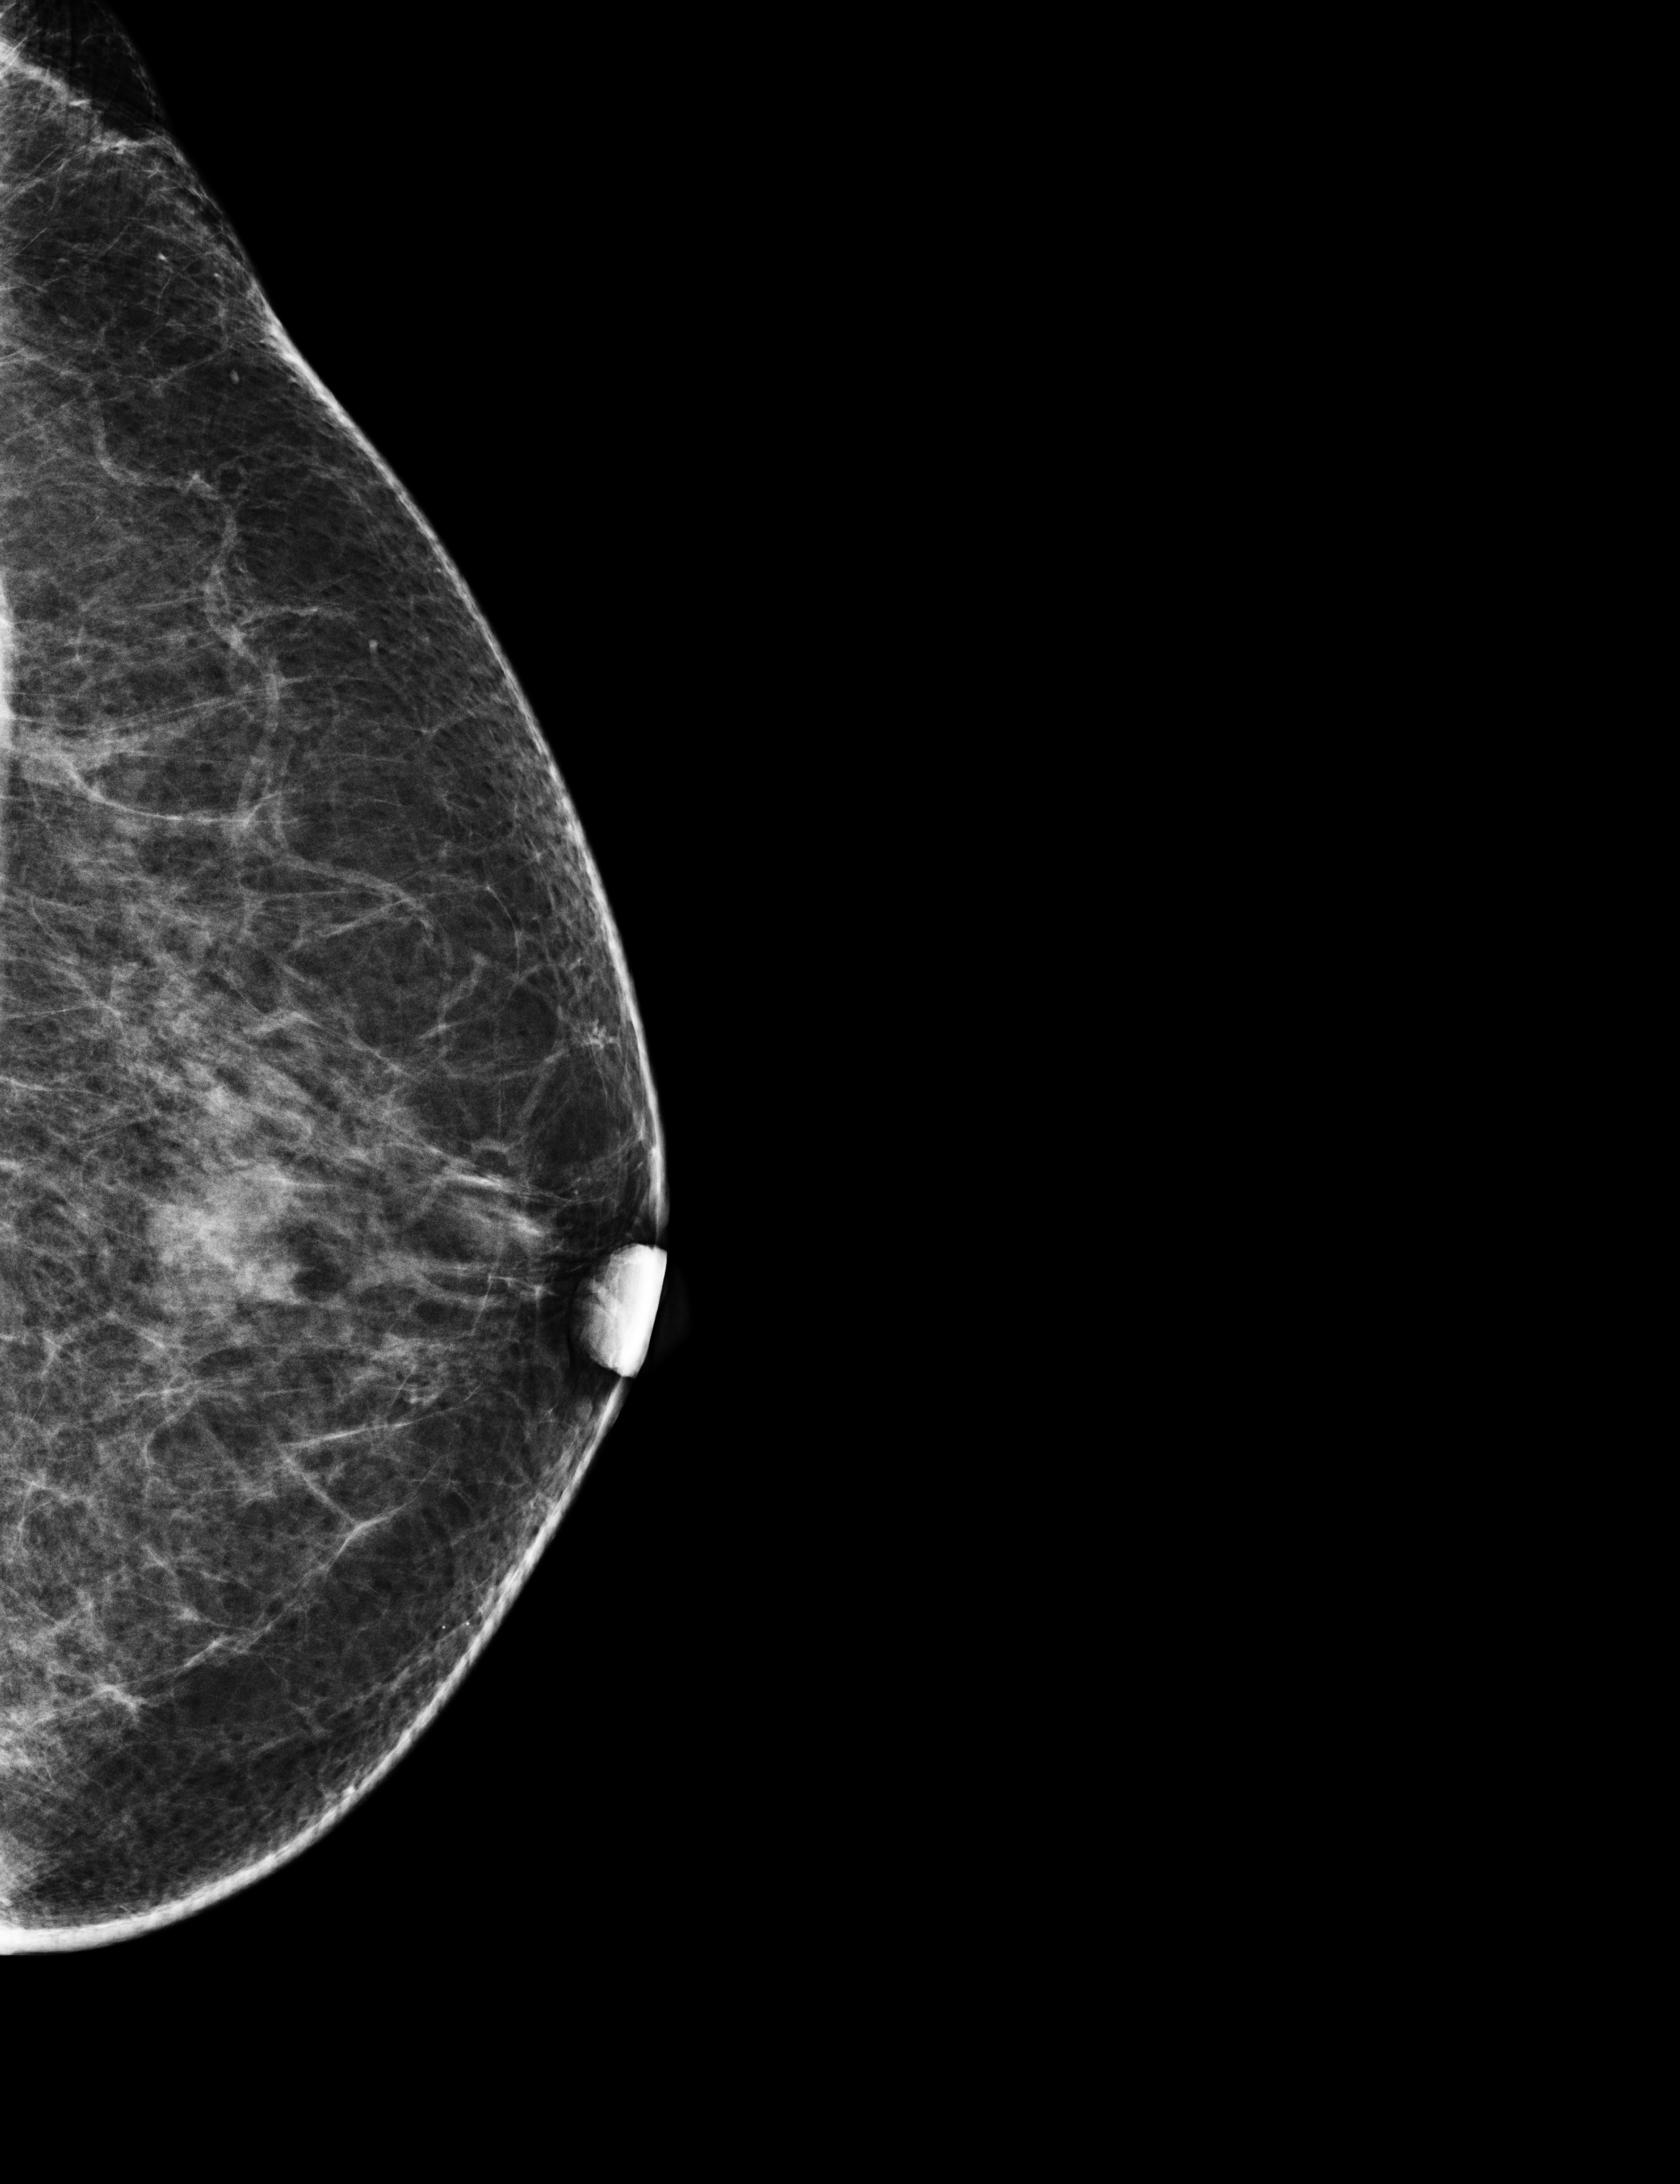
Full-field digital mammogram (FFDM); left breast; craniocaudal (CC) view; screening examination. Patient aged 61 years (female).
BI-RADS breast density category at the screening exam (both breasts, scale 1–4): 3. Final BI-RADS category for the screening round (tomosynthesis exam, both breasts): category 2. Recall: recalled for additional imaging after this screen.